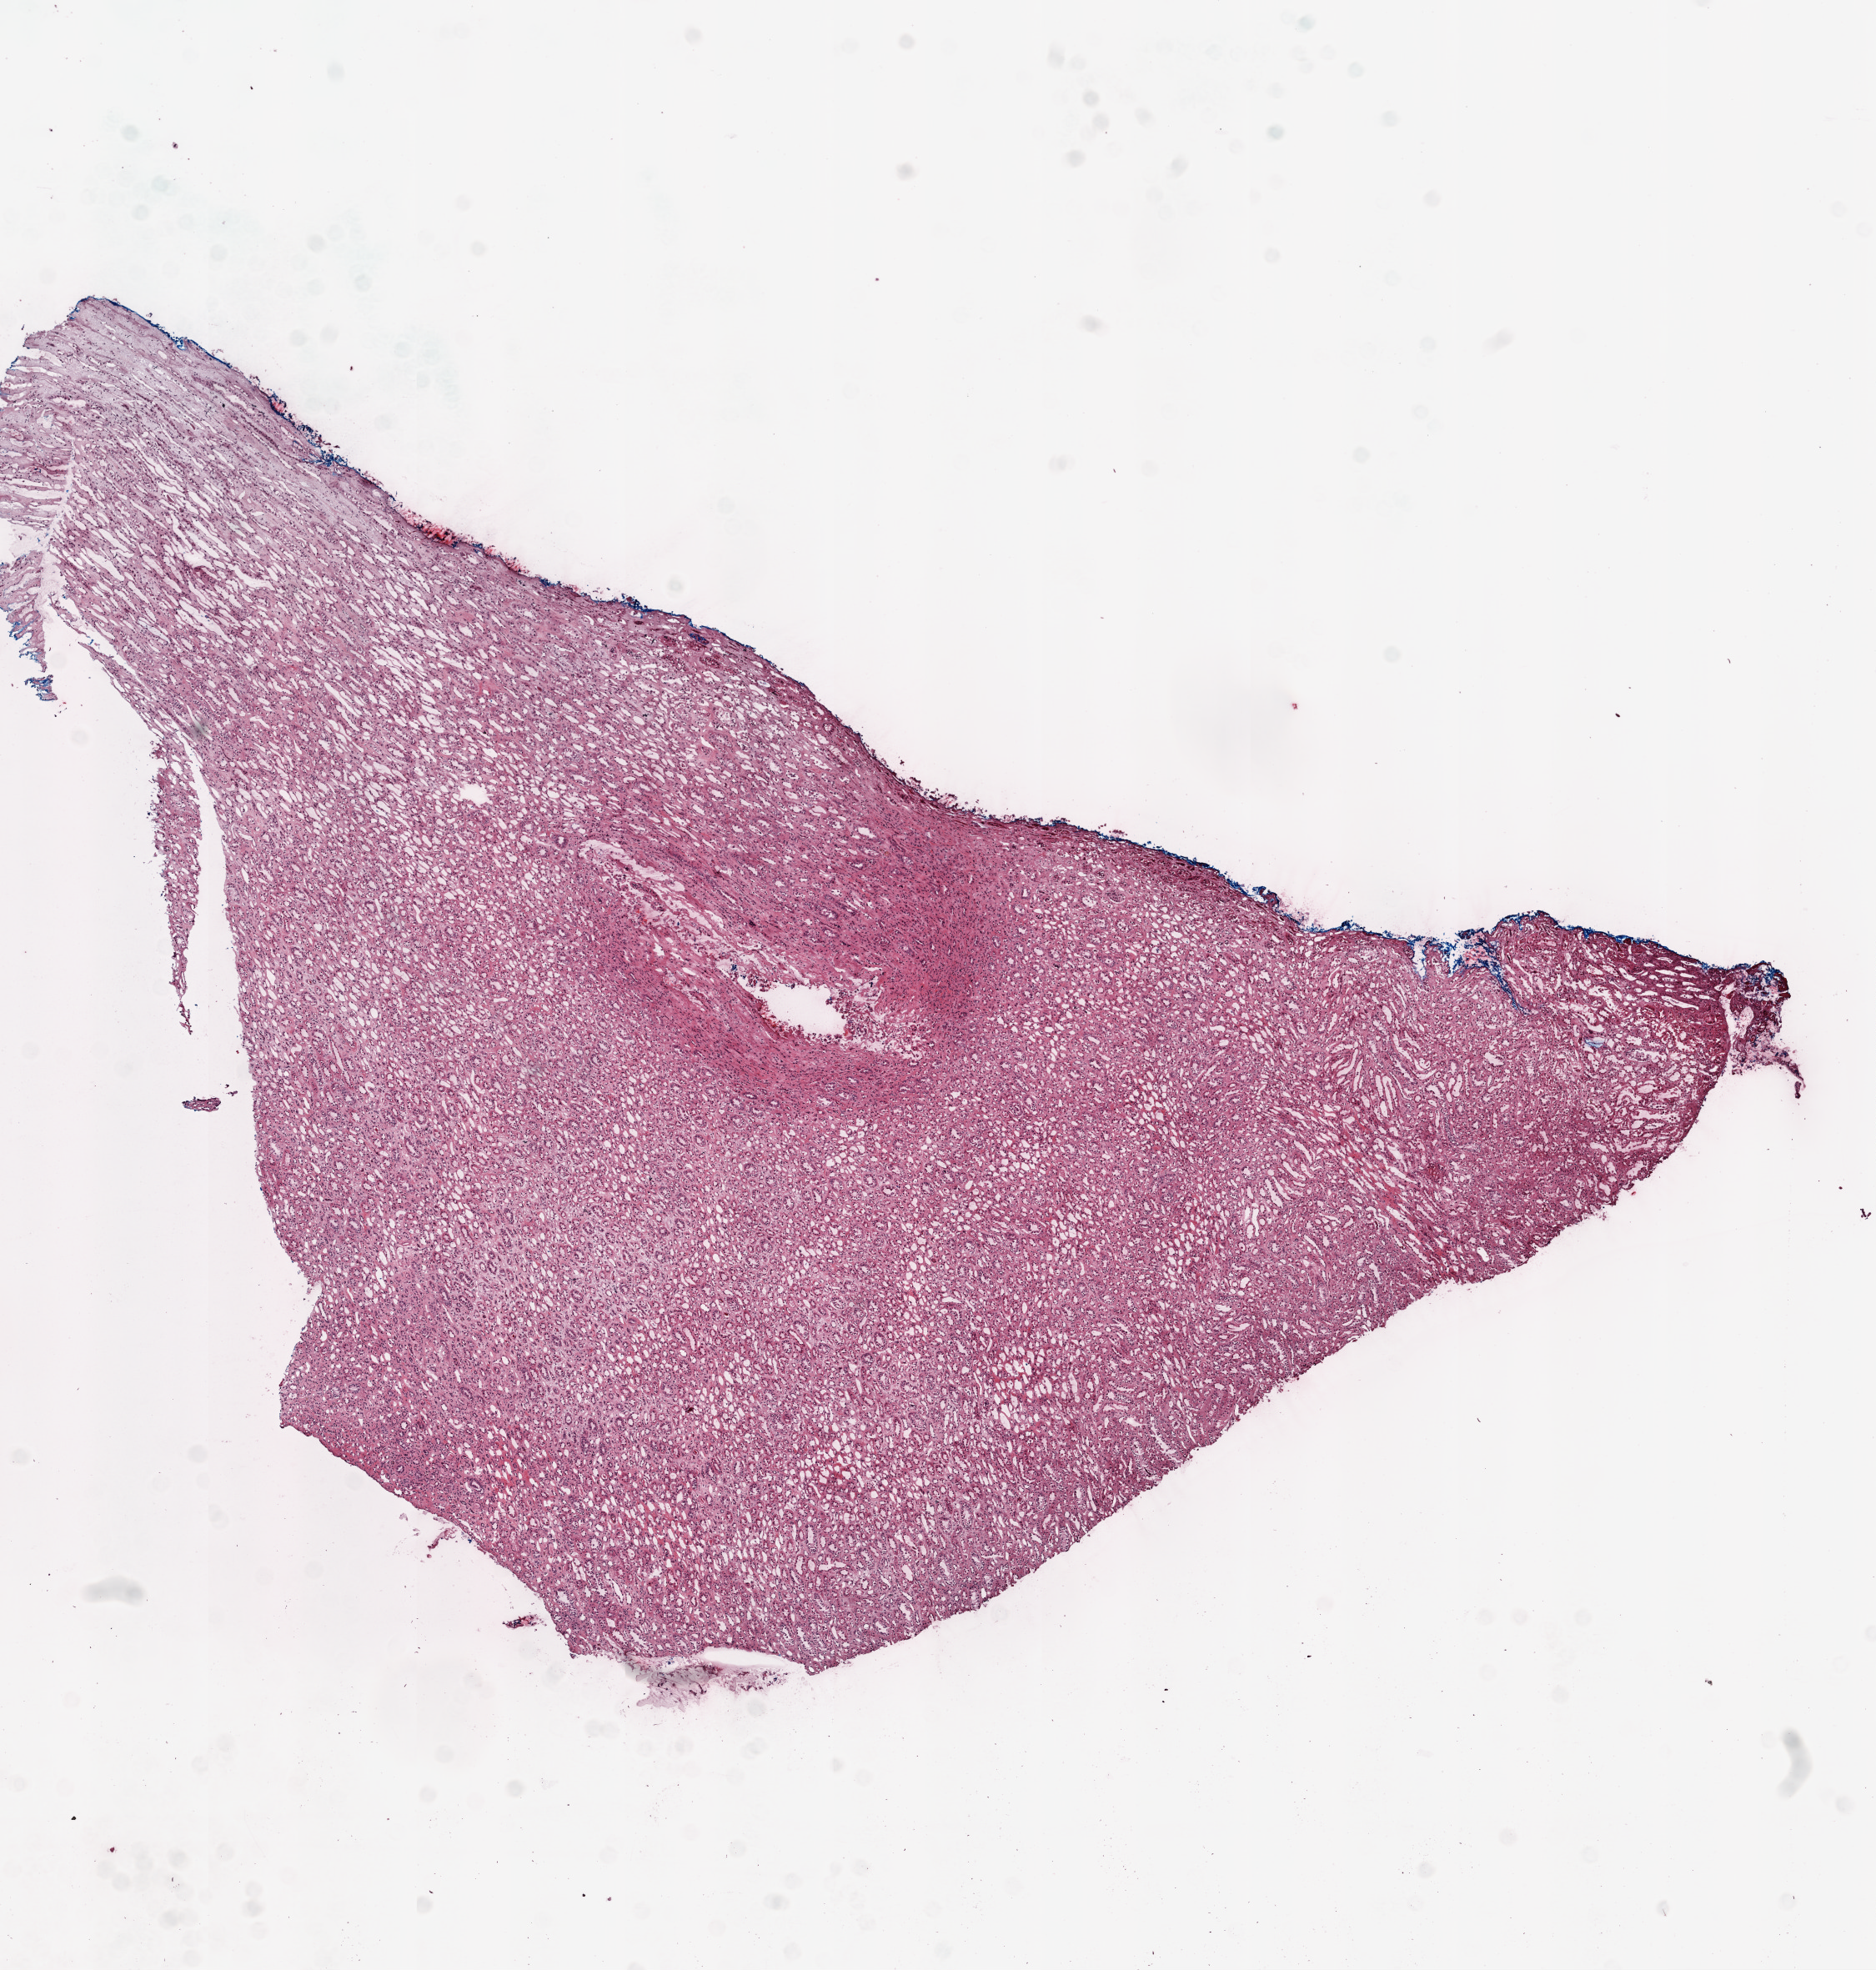
H&E-stained whole-slide image — a low-resolution overview of the entire scanned area, about 9.0 x 9.5 mm. Frozen section from the top of the tissue portion. Sample: solid tissue normal (non-tumour tissue), kidney. Patient: female, age at initial diagnosis 43 years.
This section: solid tissue normal (non-tumour) sample from the same patient. Patient diagnosis: Clear cell adenocarcinoma, NOS.